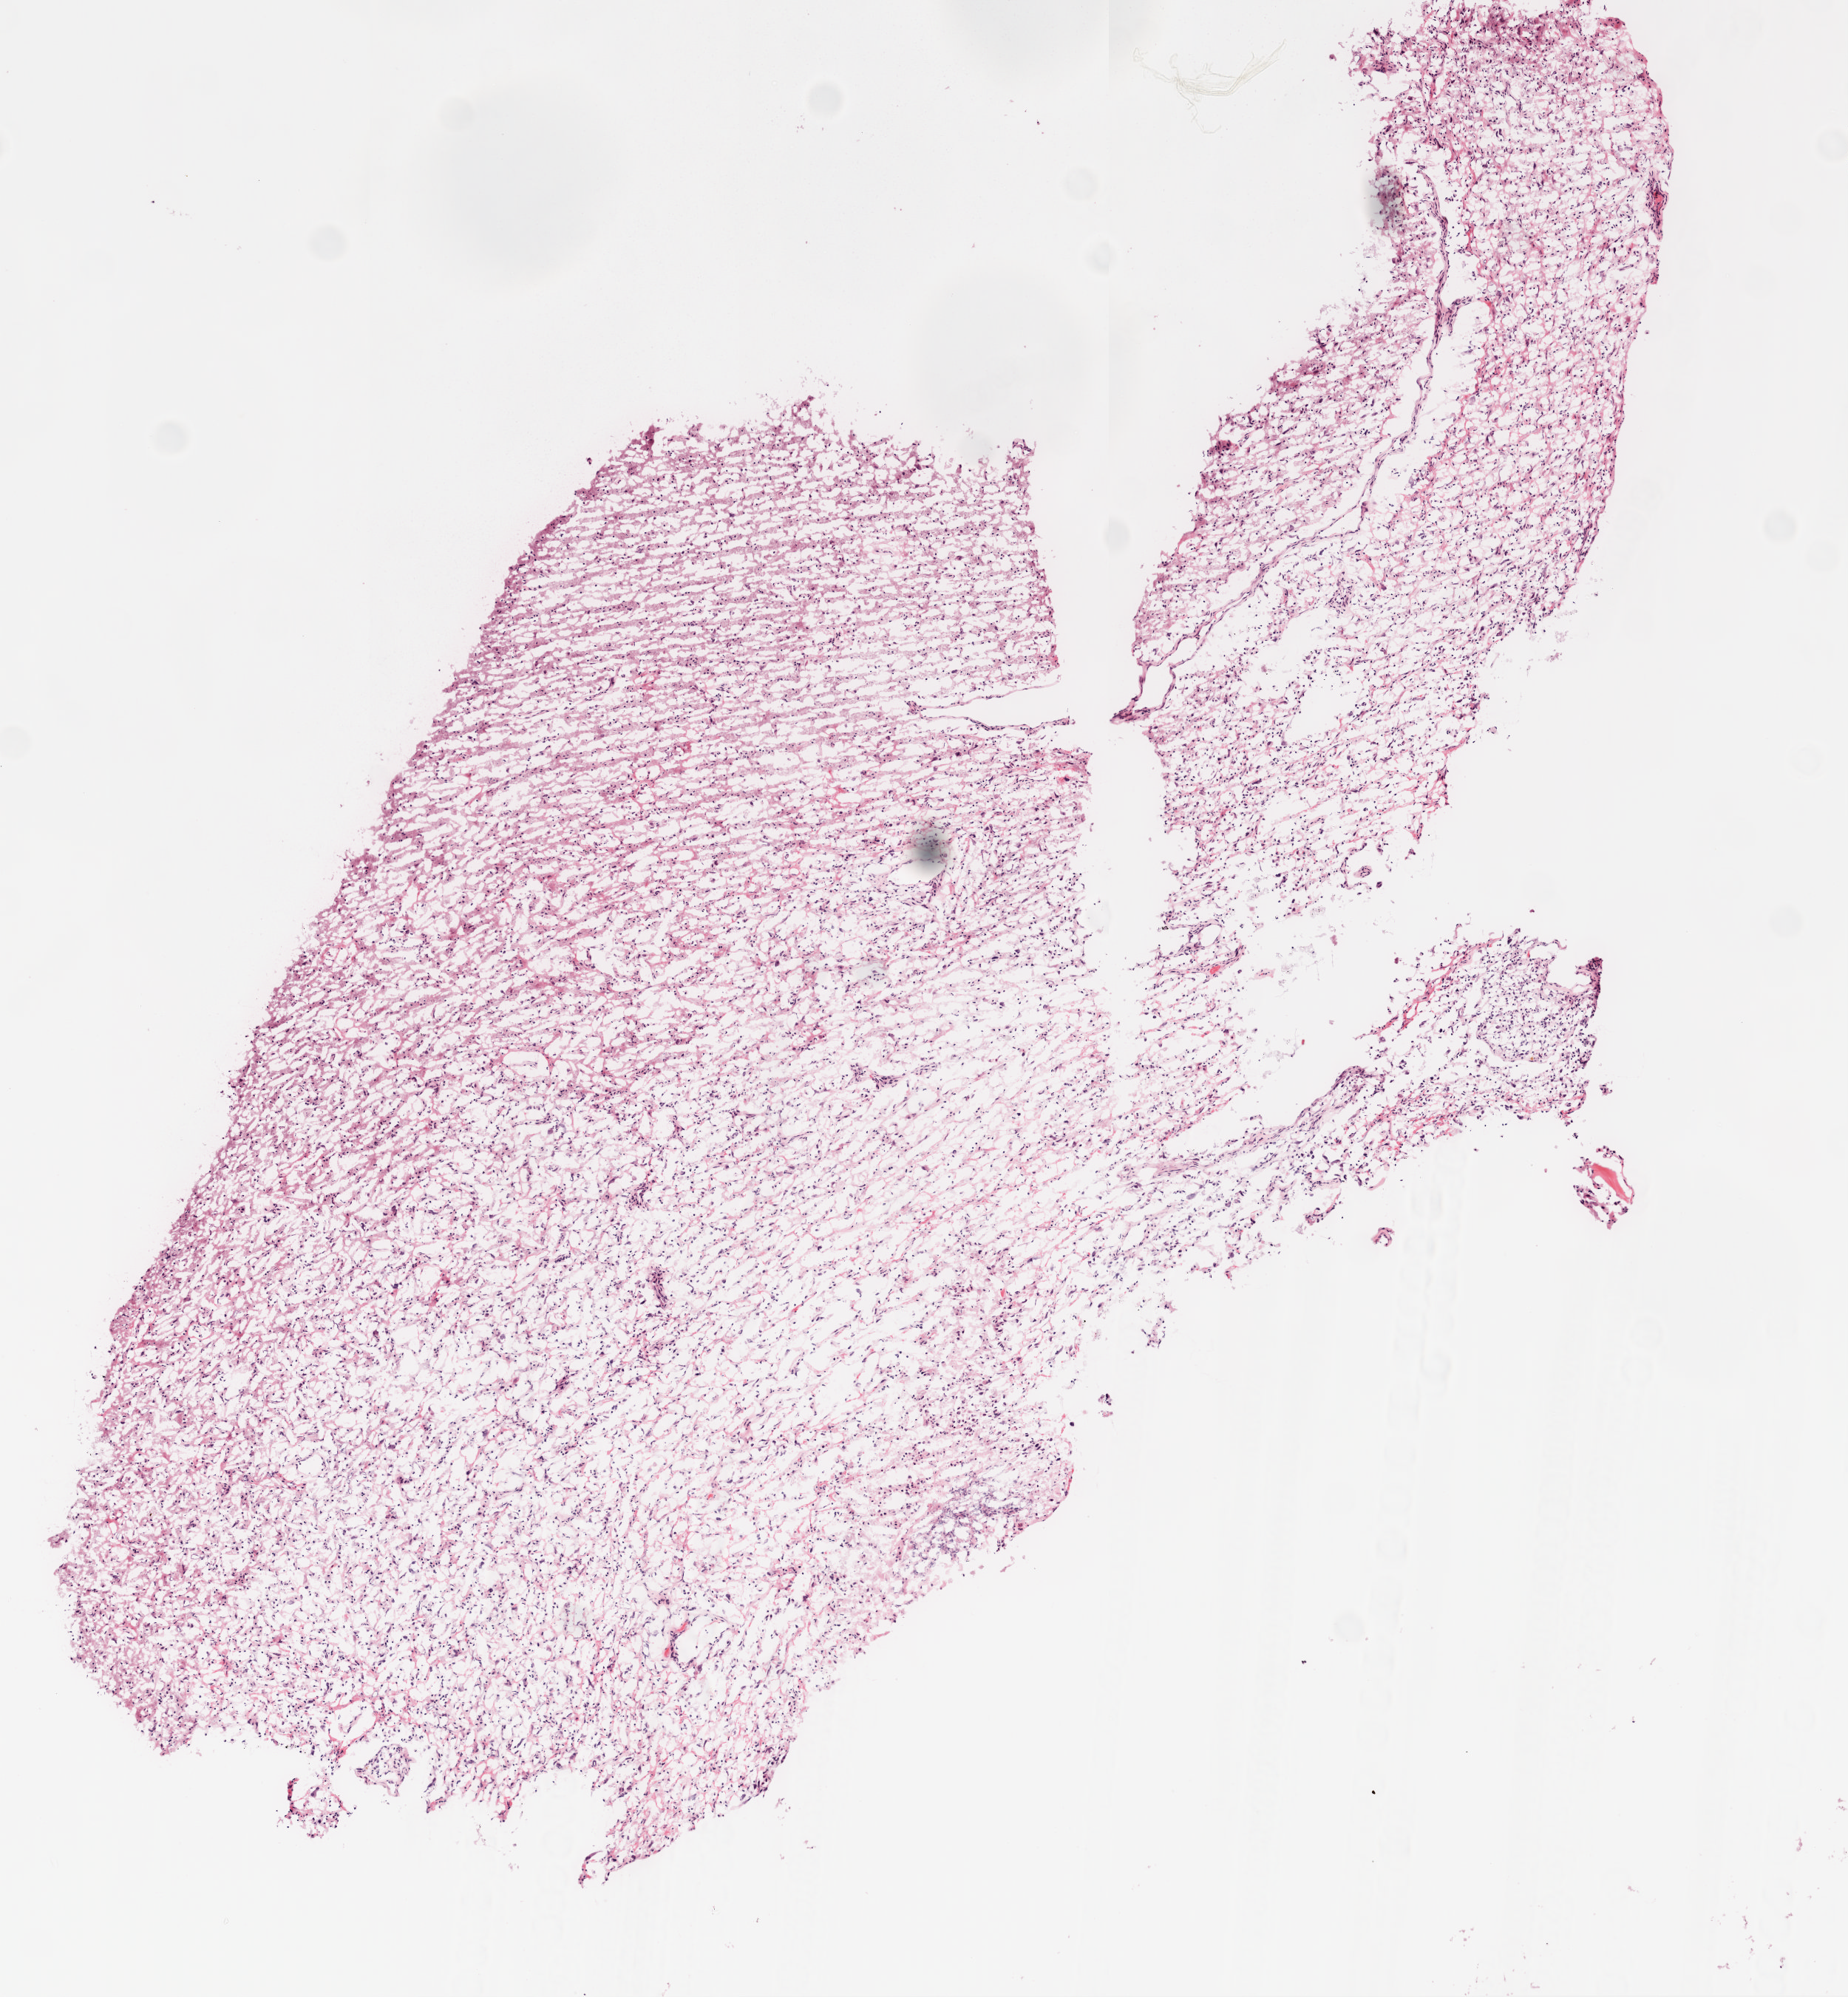
Whole-slide histology image, Hematoxylin and eosin (H&E) stained — whole scanned area (about 5.0 x 5.4 mm, acquisition: 20x scan) shown as a low-resolution overview. Frozen section from the top of the tissue portion. Brain, primary tumour sample. Patient: male, age at initial diagnosis 51 years. Pathologist review of this section (percent, as recorded): tumour cells 100%, tumour nuclei 100%, normal cells 0%, stromal cells 0%, necrosis 0%.
Histologic diagnosis: Glioblastoma.